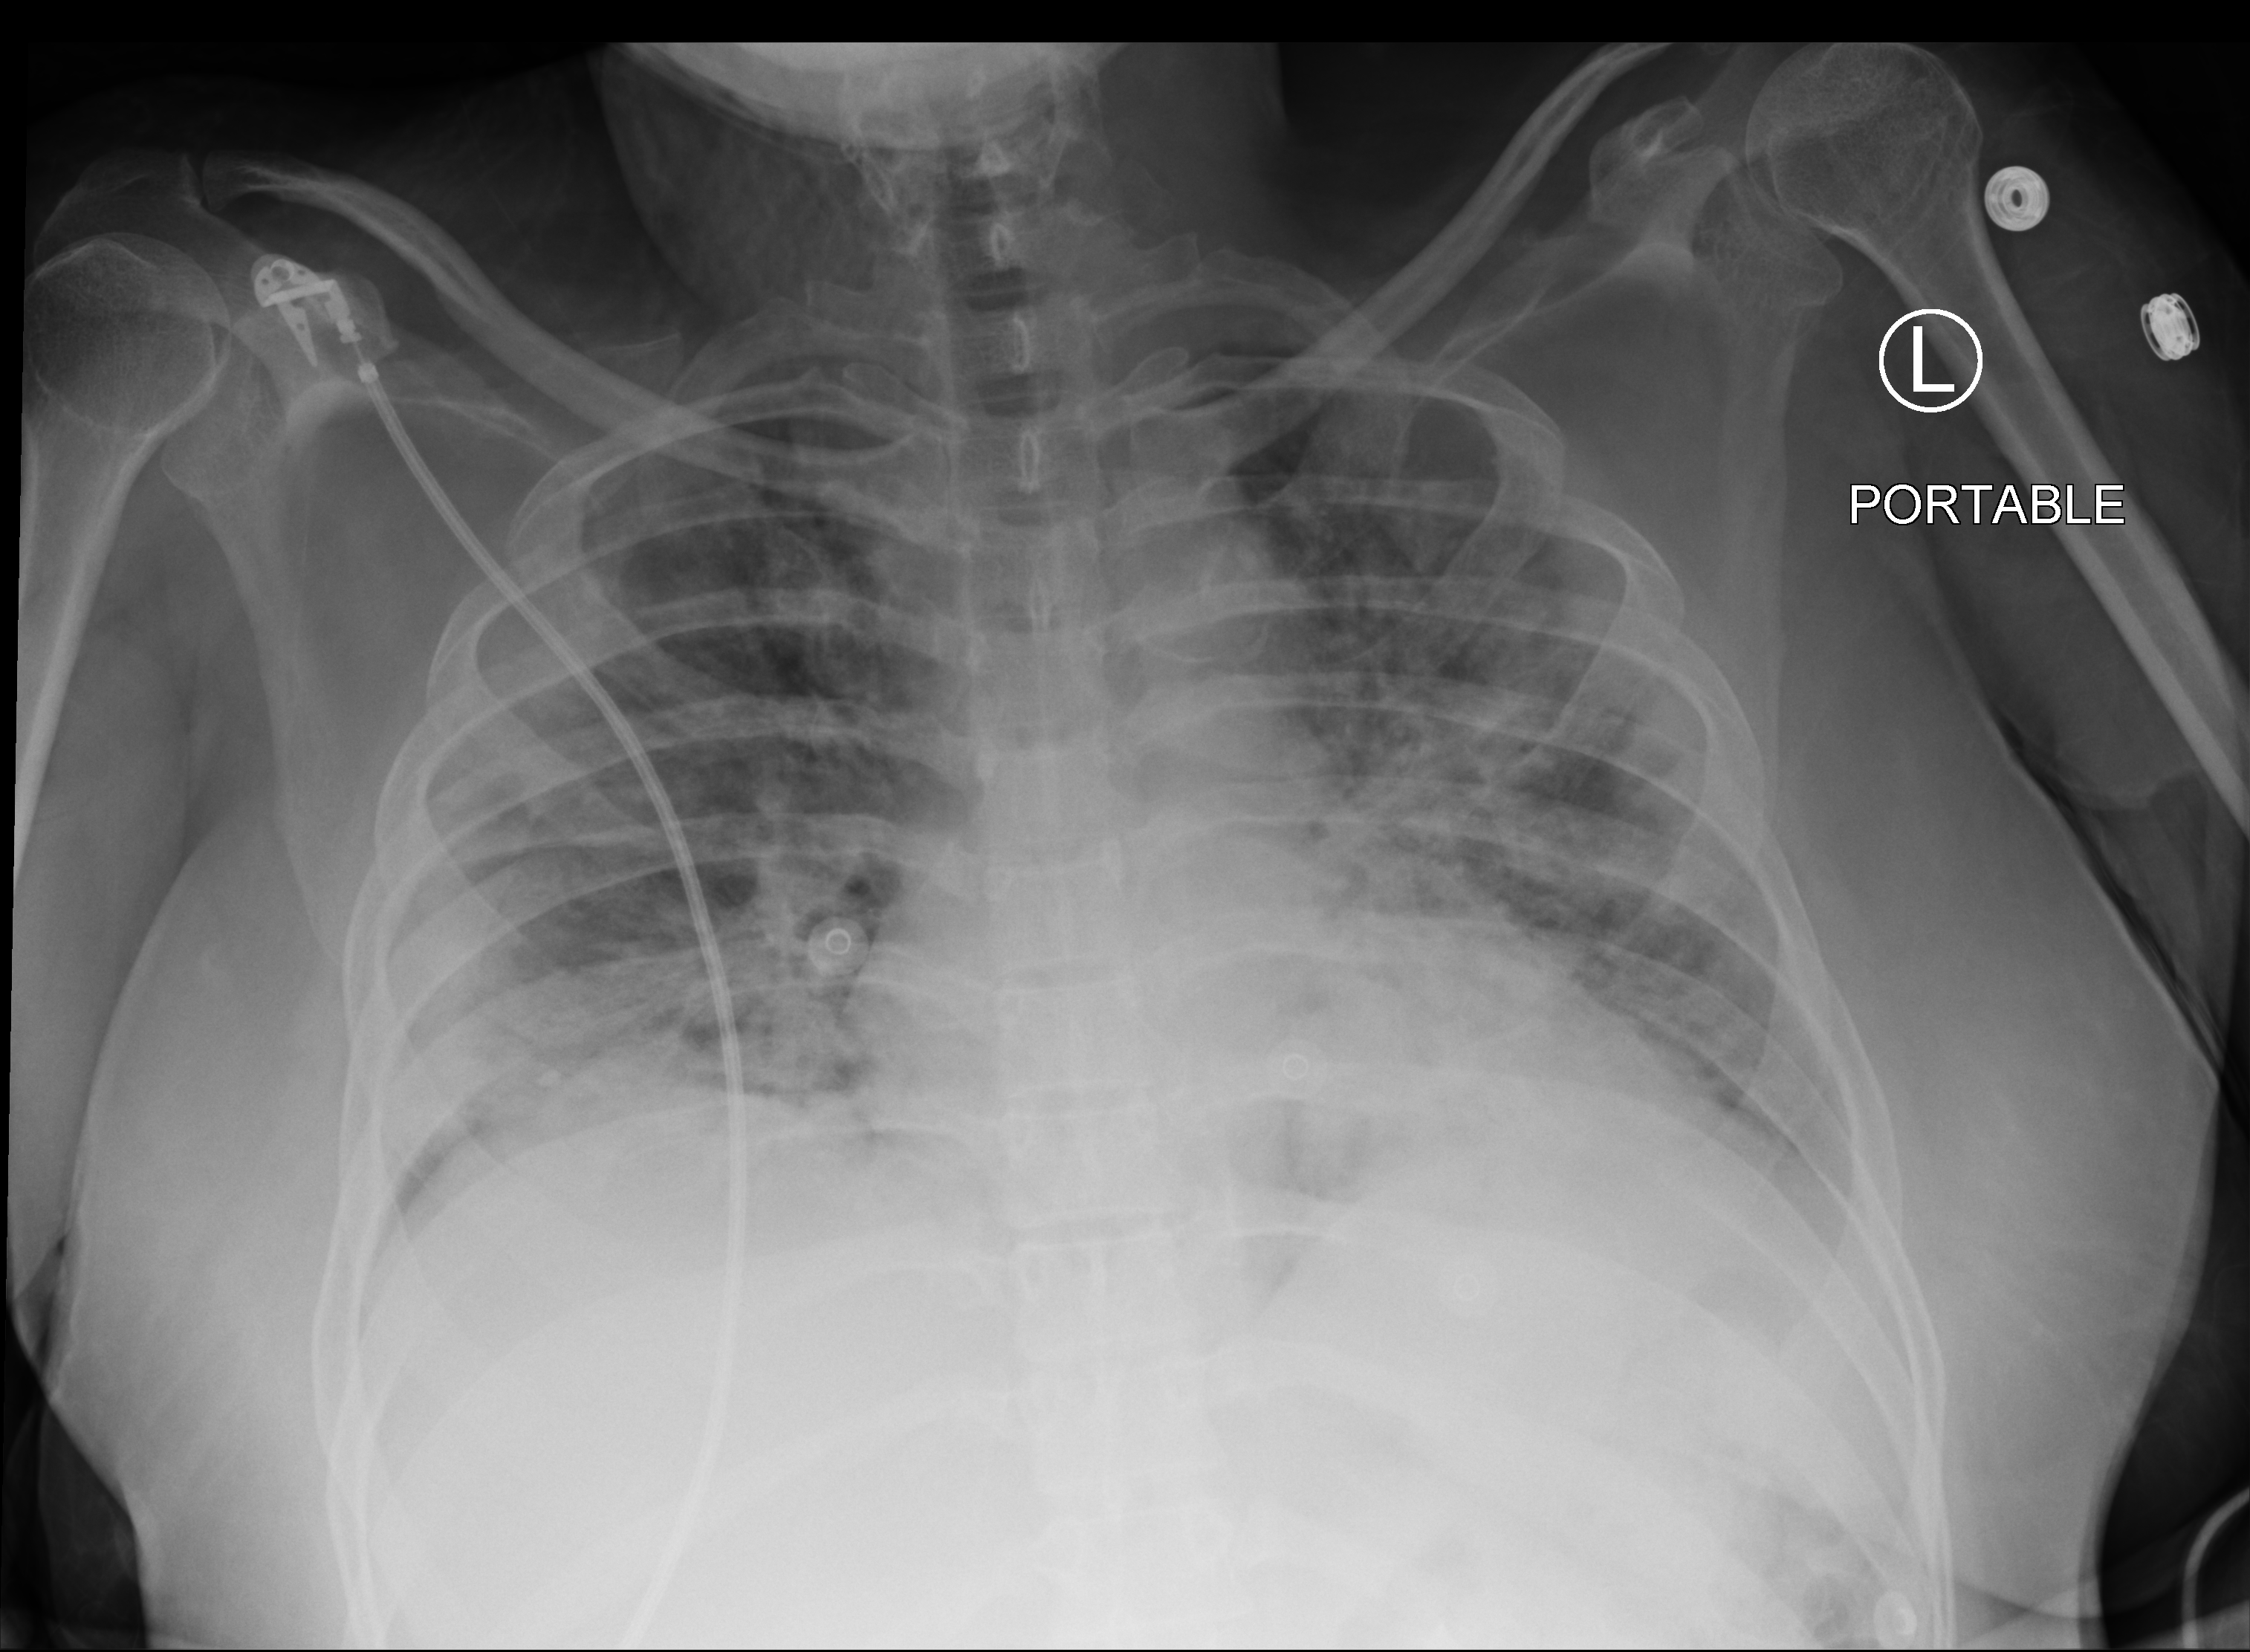
Bedside chest radiograph (computed radiography), anteroposterior (AP) projection. Patient hospitalised with COVID-19, aged 18–59 years.
Admission-level facts for this patient (not findings on this image; timing relative to this image not recorded): smoking status (admission record): never; length of hospital stay: 15 days; admitted to intensive care during this hospital stay: yes.